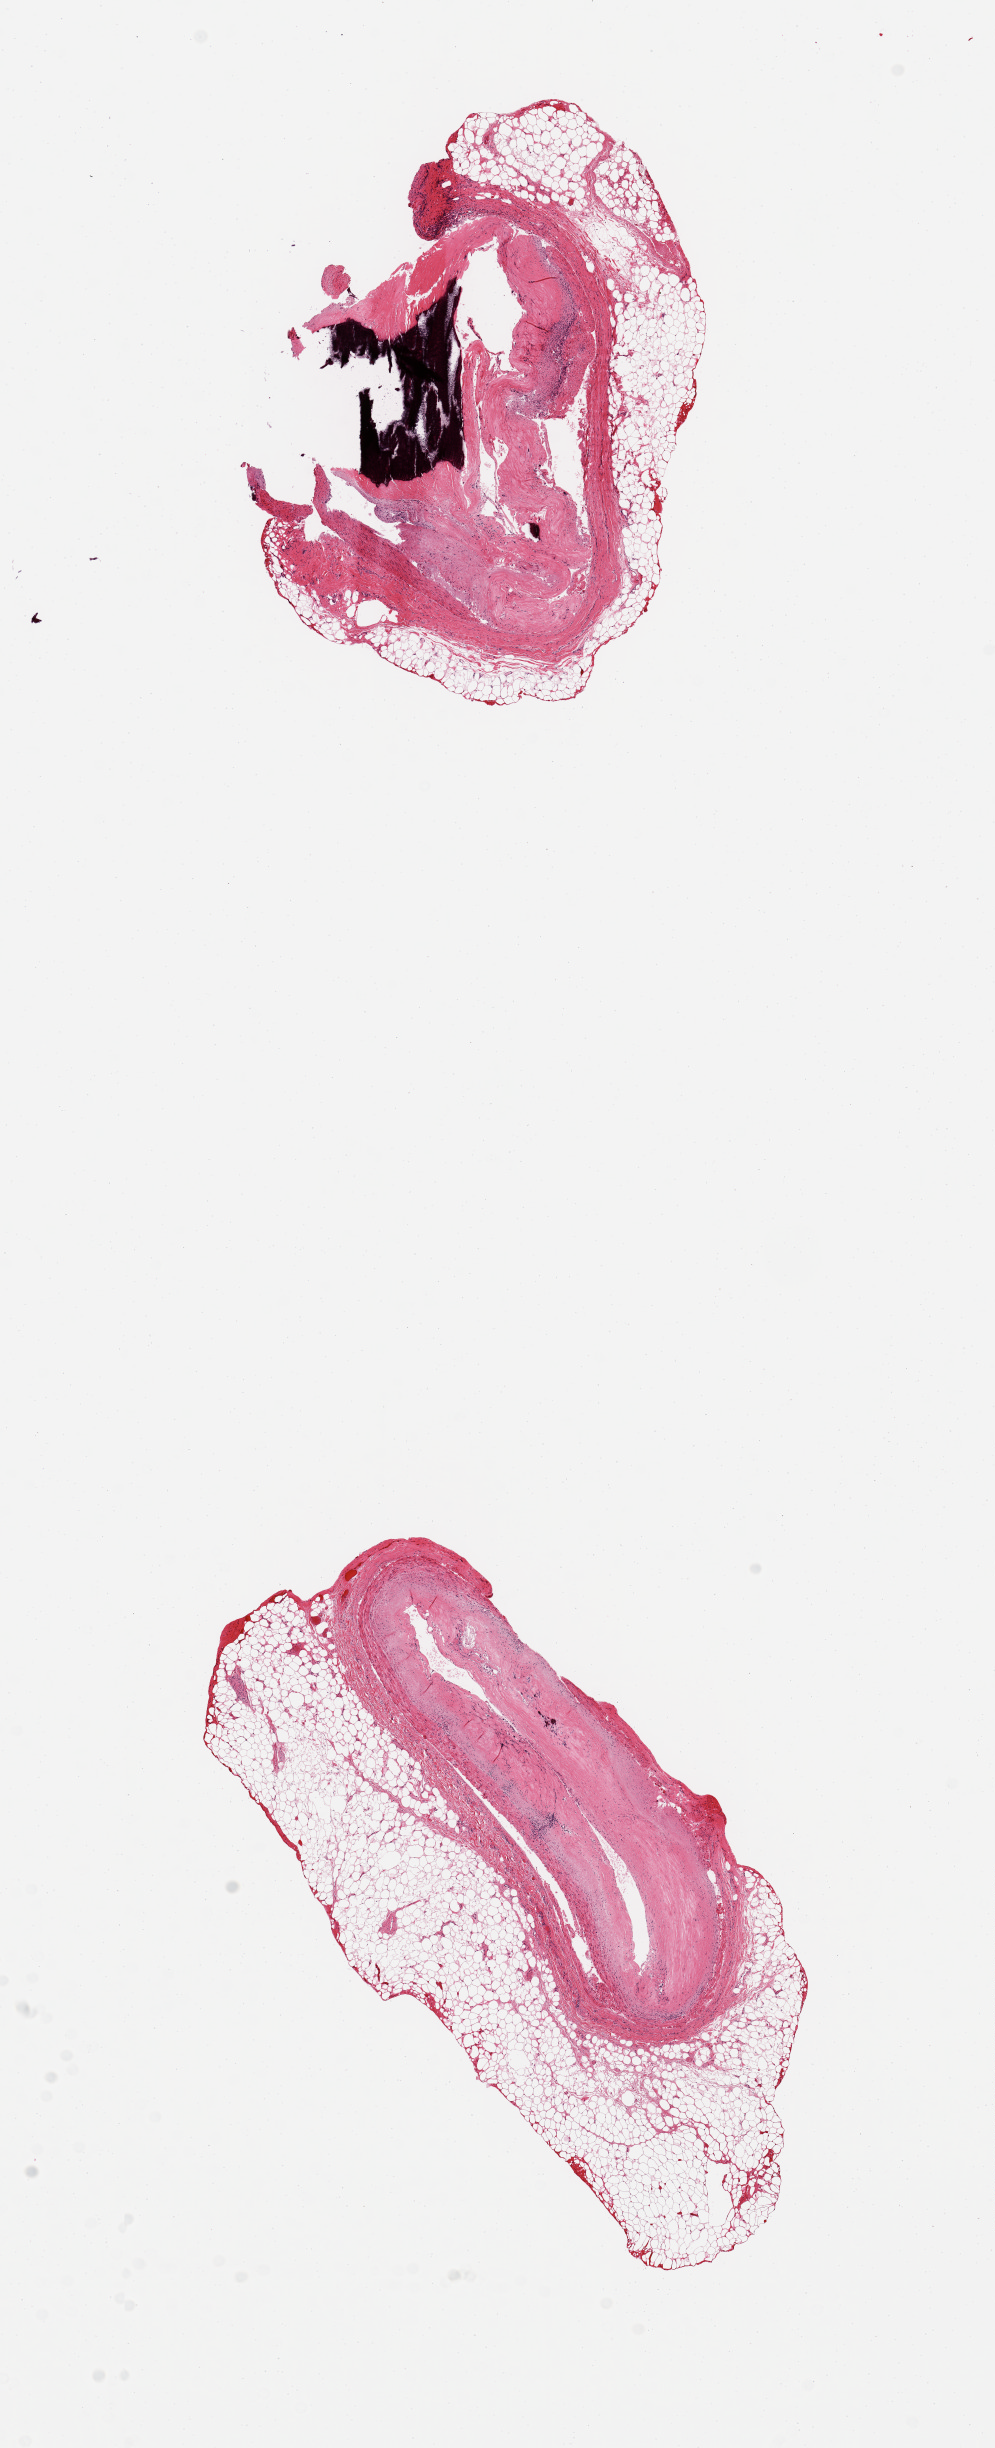
Digitized haematoxylin and eosin-stained section, brightfield, shown as a low-resolution overview of the whole scanned area (about 7.9 x 19.4 mm). PAXgene-fixed, paraffin-embedded tissue. Target tissue: coronary artery. Tissue donor sample. Donor sex: male.
Review note (as recorded): 2 pieces; severe calcific sclerotic plaques with up to 1.6 mm external [untrimmed] fat.